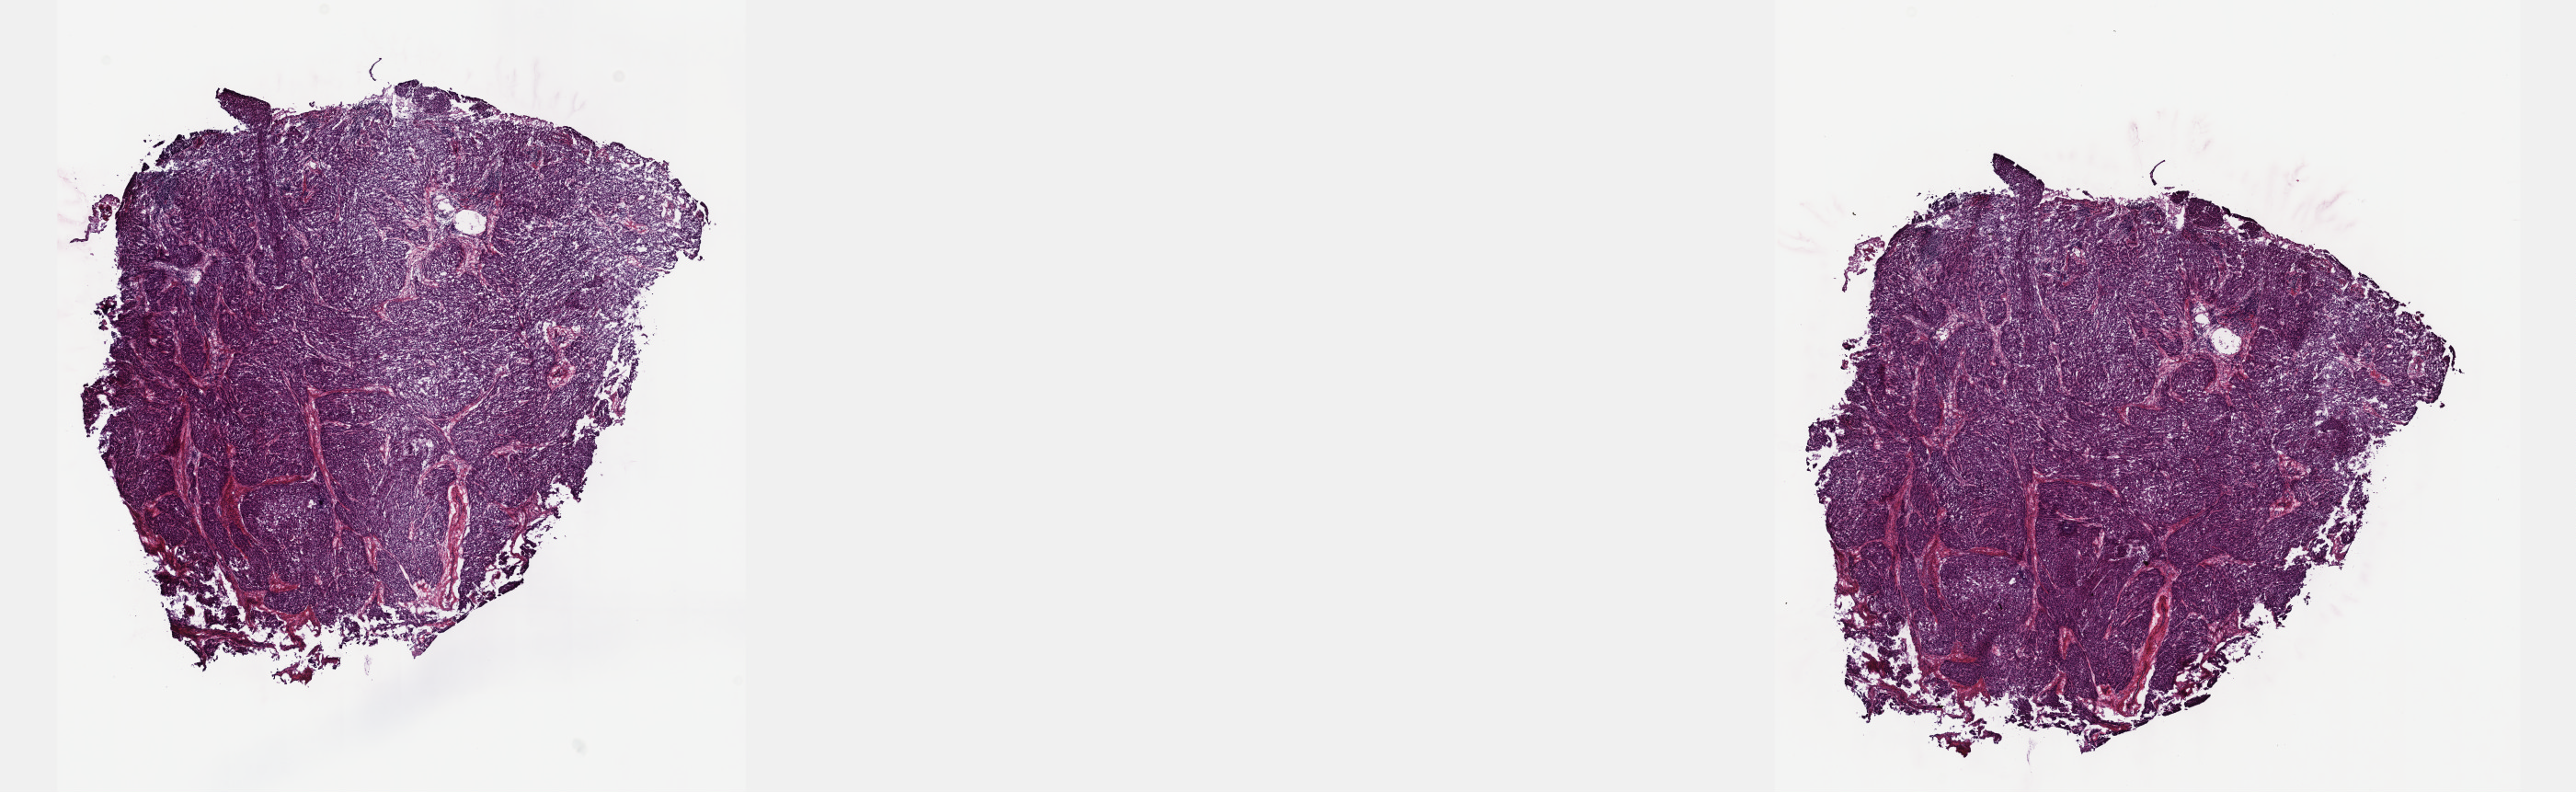
Hematoxylin and eosin (H&E) stained whole-slide image, shown as a low-resolution overview of the whole scanned area (about 22.6 x 7.0 mm), frozen section from the top of the tissue portion, cervix, primary tumour sample. Patient: female, age at initial diagnosis 67 years. Pathologist review of this section (percent, as recorded): tumour cells 90%, tumour nuclei 90%.
Pathologic diagnosis: Squamous cell carcinoma, large cell, nonkeratinizing, NOS (cervix uteri).